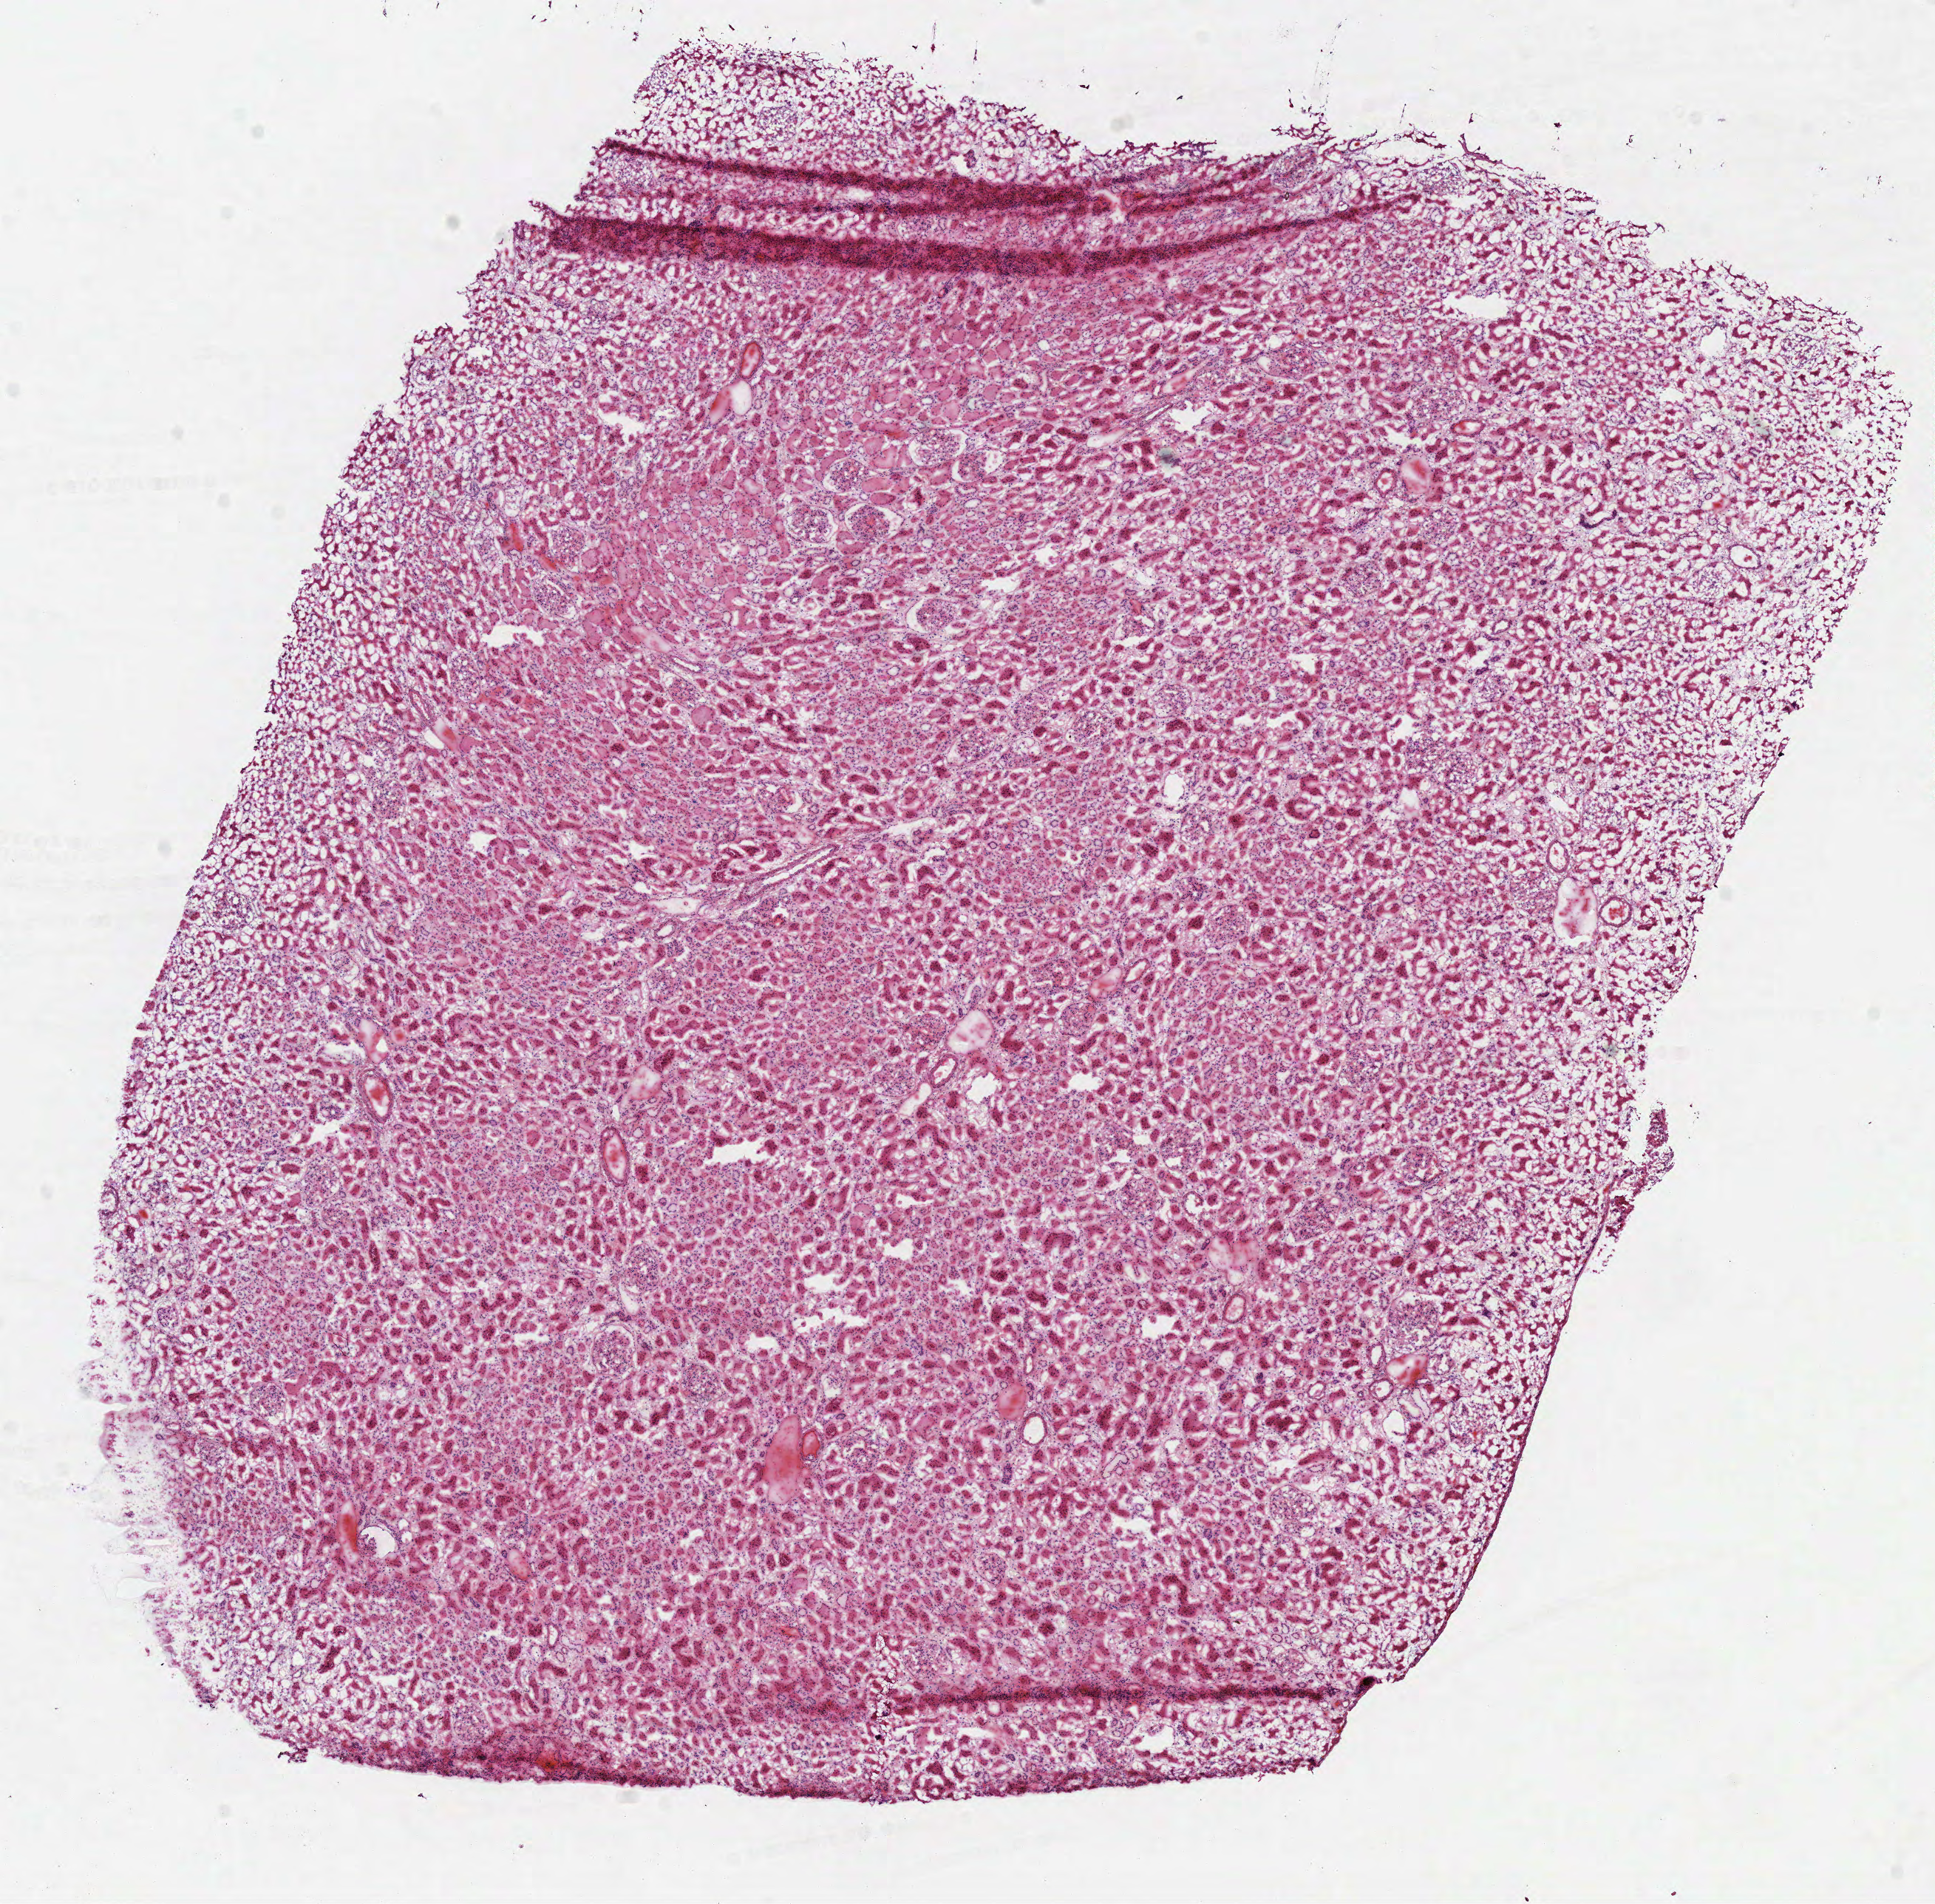
Digitized Hematoxylin and eosin (H&E) stained tissue section (whole slide), a low-resolution overview of the entire scanned area, about 10.3 x 10.1 mm (from a 40x scan); frozen section from the top of the tissue portion; solid tissue normal (non-tumour tissue) sample from the kidney. Male, age 32 years at initial diagnosis.
This section: solid tissue normal sample (biorepository sample class). Patient diagnosis: Clear cell adenocarcinoma, NOS.